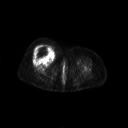
FDG PET of an extremity soft-tissue mass (from a PET/CT study), one axial slice; slice 49 of 267 in the series (ordered by position); 3.27 mm slice thickness; 128 × 128 image matrix, field of view 700 × 700 mm. Female patient, age 56 years. From the clinical record (not read from this slice): histological type: malignant solitary fibrous tumor; grade: intermediate; site of the primary tumour: right thigh.
Annotated regions visible in this slice (expert contour drawn on MRI and transferred to this co-registered scan by the dataset authors):
- gross tumour volume including surrounding oedema: box from (x=31, y=45) to (x=55, y=62) px
- gross tumour volume (mass): (x=32, y=45)–(x=55, y=62)